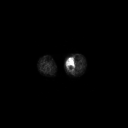
FDG PET of an extremity soft-tissue mass (from a PET/CT study), one axial slice; slice 135 of 223 in the series (ordered by position); 3.27 mm slice thickness; 128 × 128 image matrix. Female patient, age 70 years. Case-level facts recorded for this patient, not image findings: histological type: extraskeletal high grade osteogenic sarcoma; grade: high; site of the primary tumour: left calf.
Annotated regions visible in this slice (expert contour drawn on MRI and transferred to this co-registered scan by the dataset authors):
- gross tumour volume (mass): bounding box <66,59,74,70> (left, top, right, bottom; pixels)